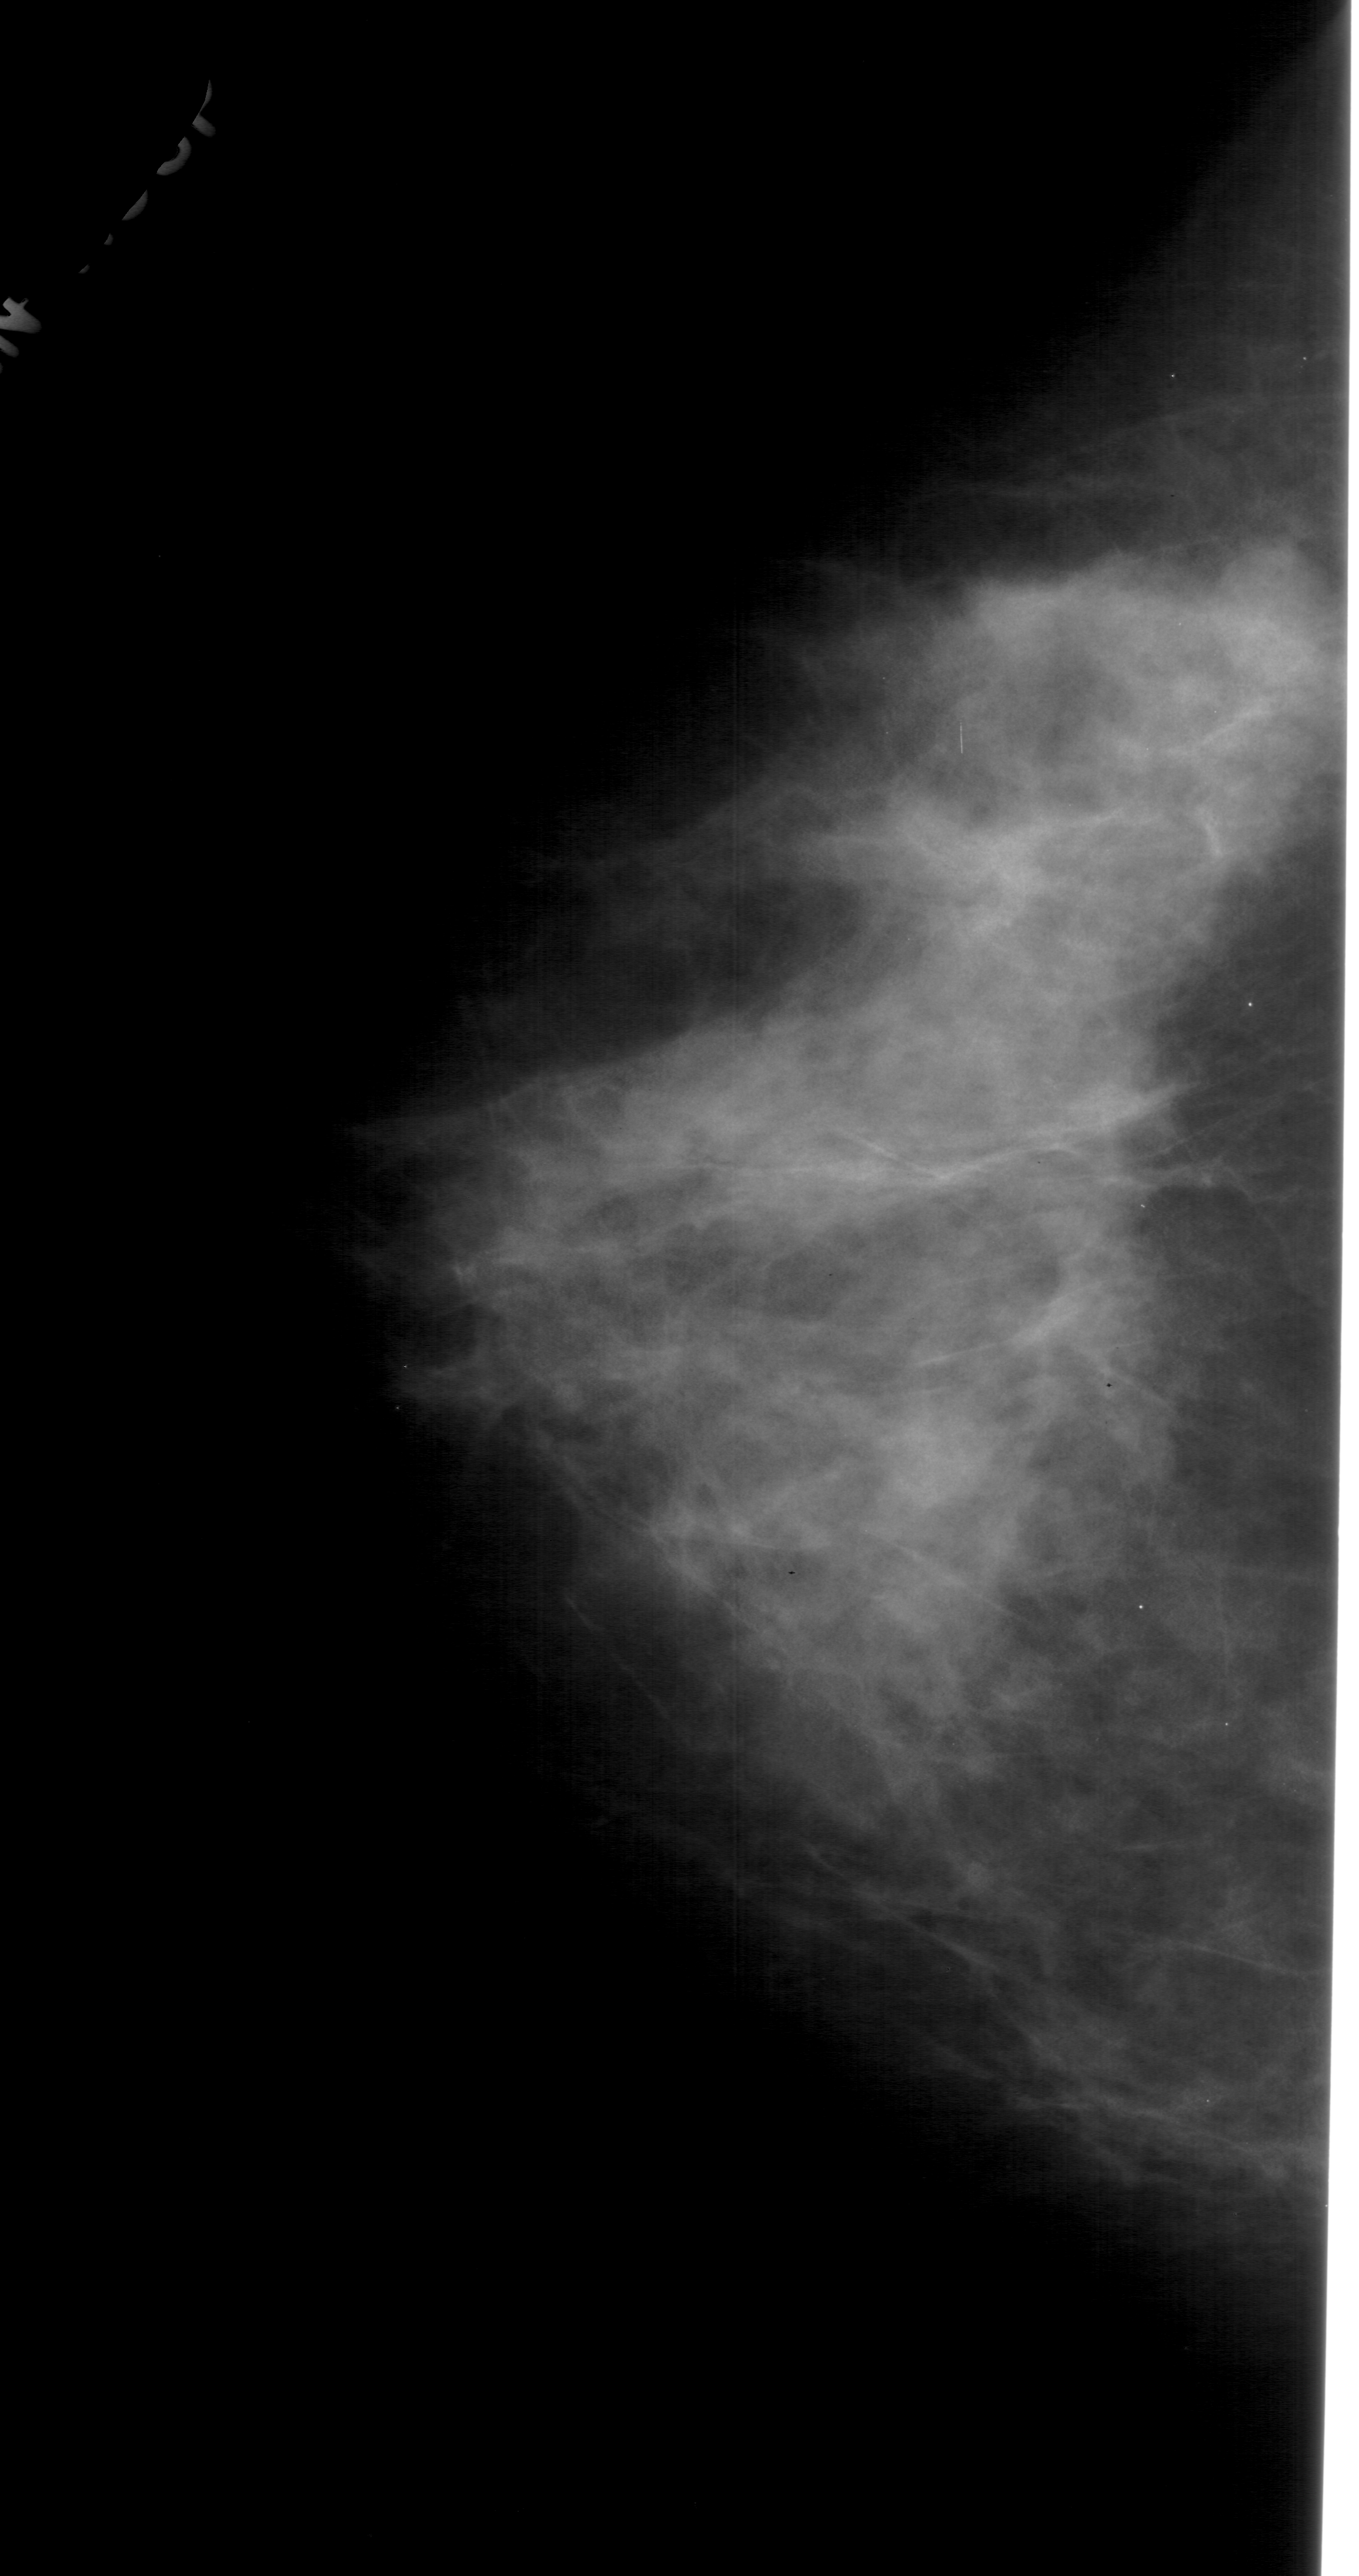
Mammogram (digitized film); left breast; CC view; BI-RADS breast density category 3 (scale 1–4); 1359 × 2576 image matrix.
Marked abnormalities (boxes around the expert regions of interest):
- mass, shape round, margins obscured; BI-RADS assessment category 4; pathology result (as recorded, not read from the image): benign: bounding box (x1, y1, x2, y2) in pixels: (1205, 525, 1326, 683)